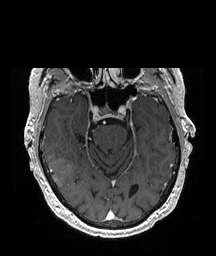
Brain MRI from a brain-tumour surgery series, one axial slice; position 139 of 208 along the scan axis; T1-weighted post-contrast; 216 × 256 image matrix, field of view 216 × 256 mm. From the clinical record (not read from this slice): histopathology: Glioblastoma; WHO grade: 4; IDH mutation: no.
Annotated regions visible in this slice (expert manual segmentation):
- tumour: bounding box (x1, y1, x2, y2) in pixels: (48, 156, 71, 186)